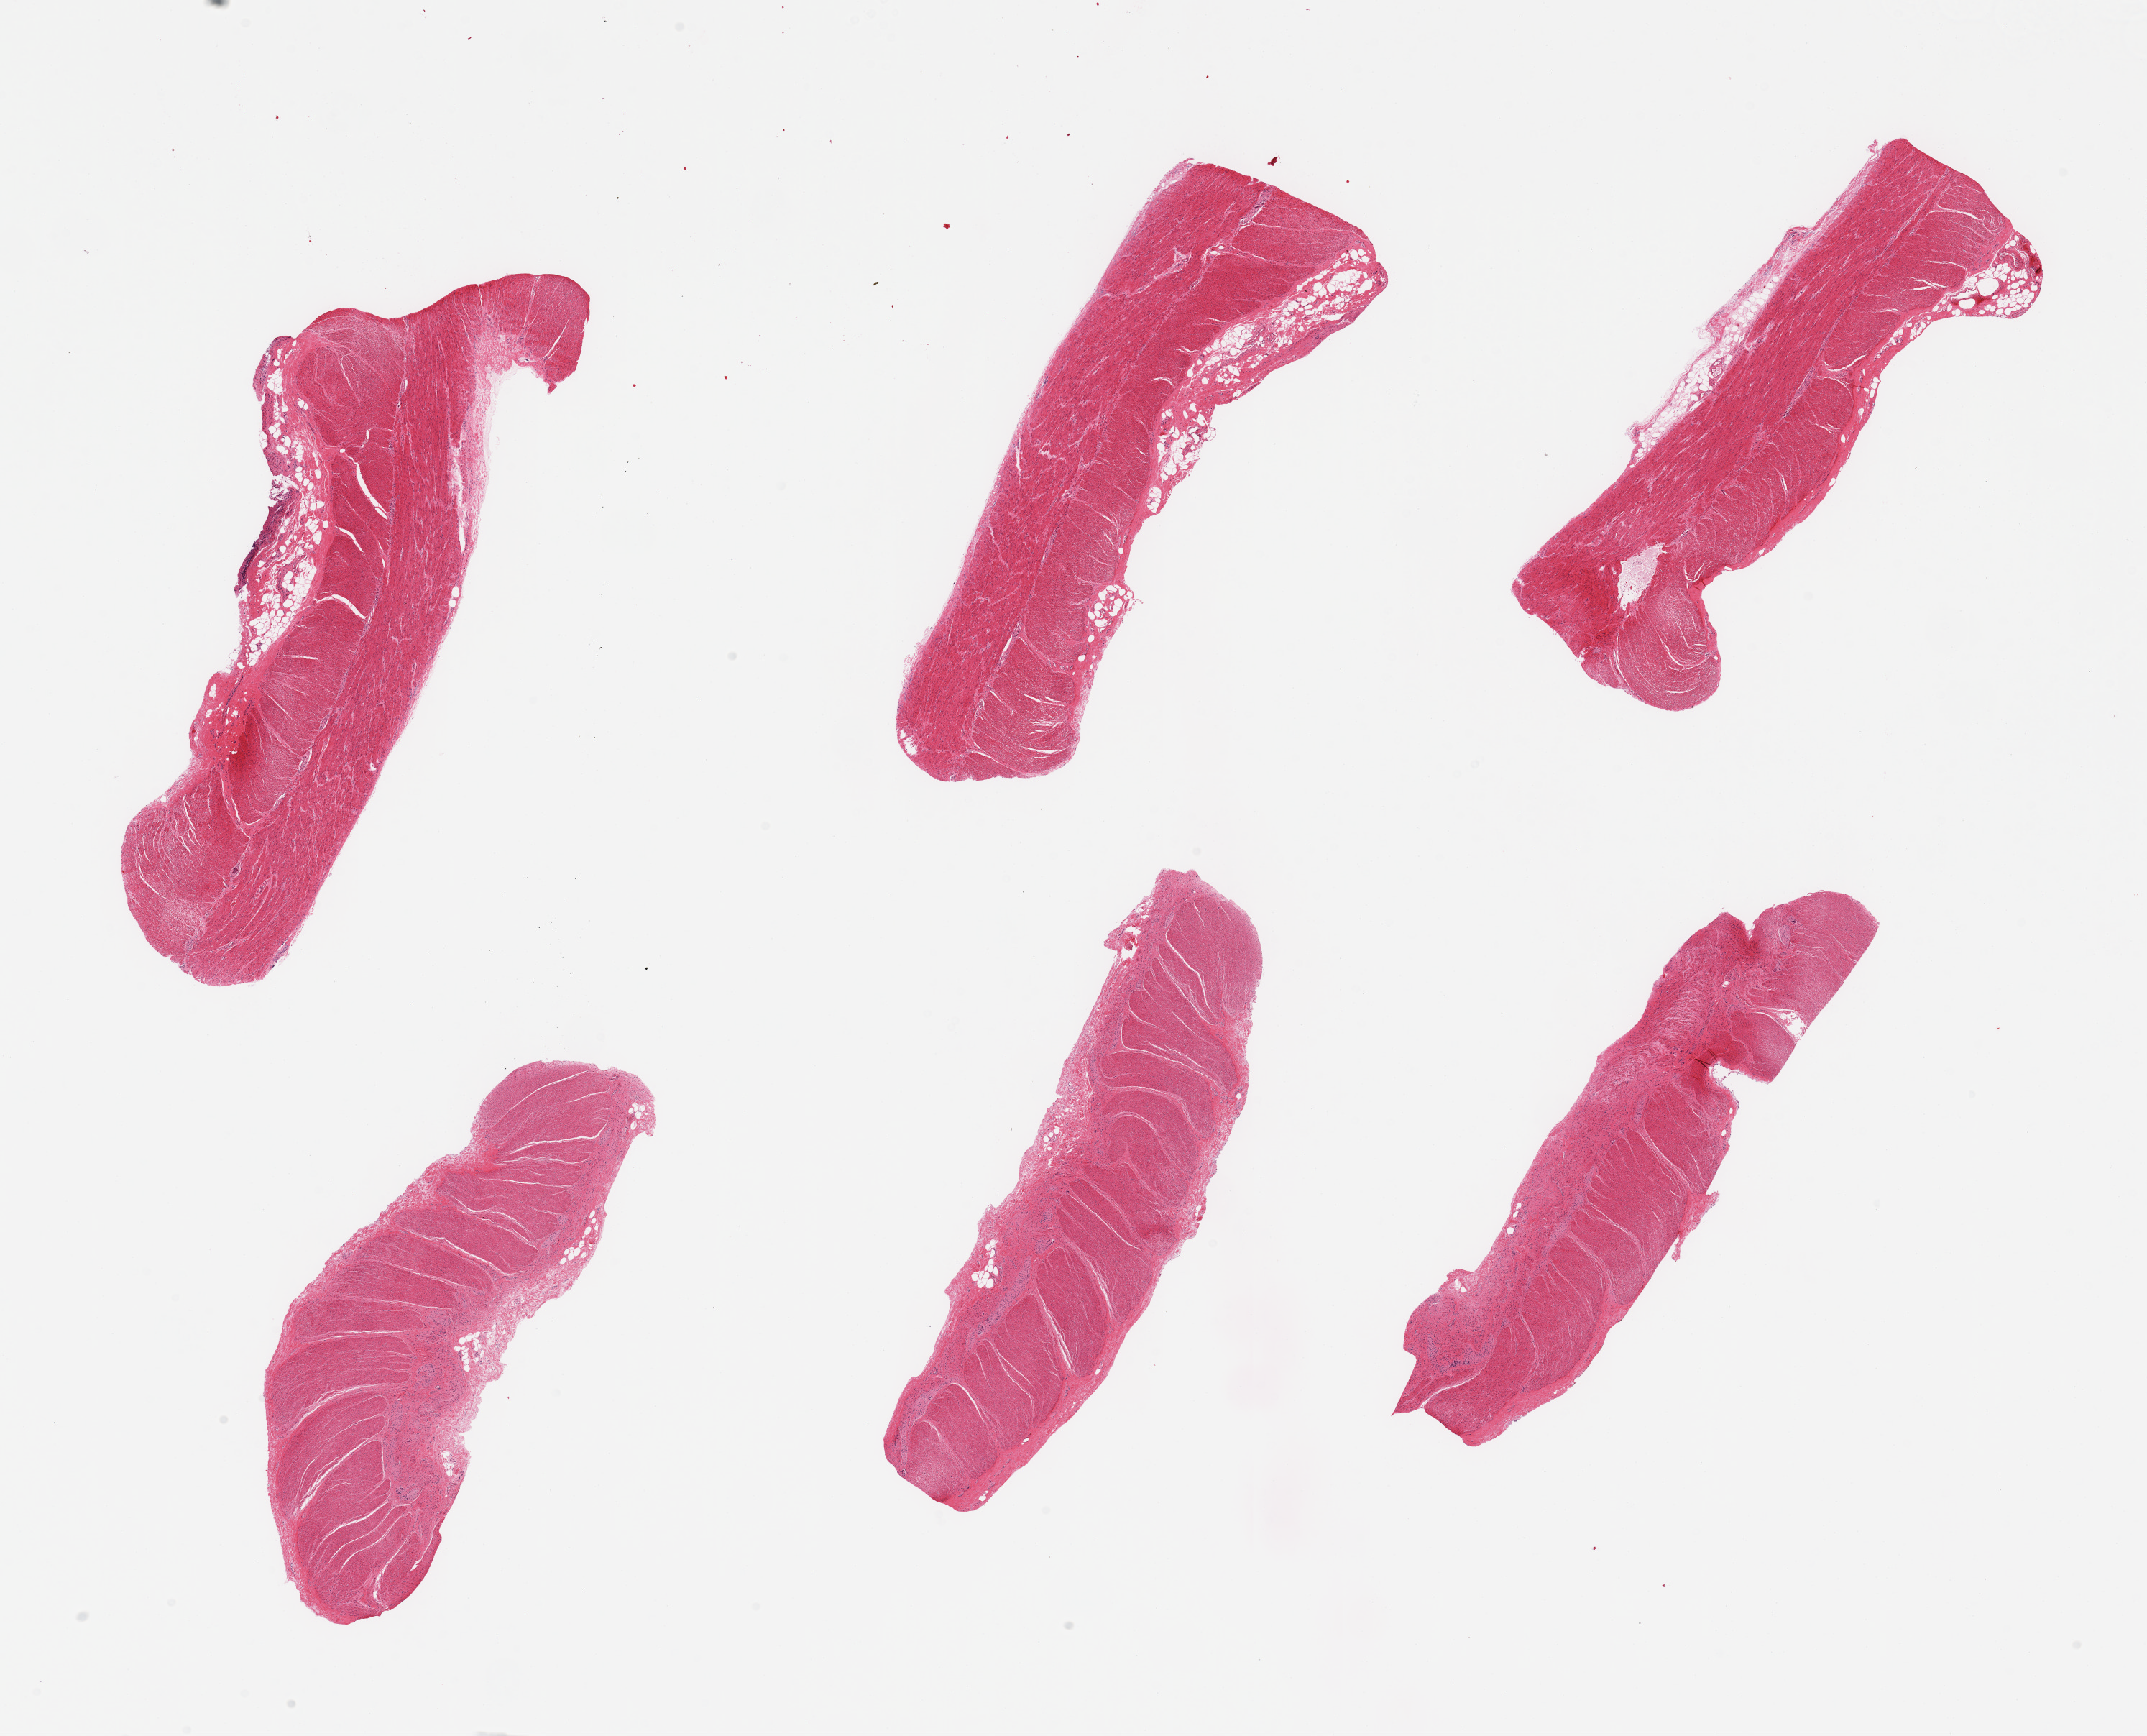
Haematoxylin and eosin whole-slide image — low-resolution overview of the scanned area, about 23.6 x 19.1 mm (from a 20x scan). PAXgene-fixed paraffin-embedded (PFPE) section. Section of sigmoid colon (target tissue). Tissue donor sample. Donor: male.
• review note (as recorded): 6 pieces, confirmed target muscularis